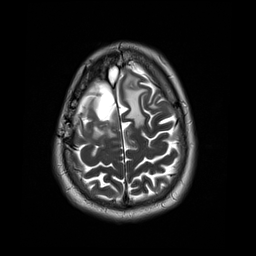
Brain MRI from a brain-tumour surgery series, one axial slice. Position 9 of 44 along the scan axis. 4 mm slice thickness. 256 × 256 image matrix, field of view 240 × 240 mm. Case-level facts recorded for this patient, not image findings: histopathology: Astrocytoma; WHO grade: 4; IDH mutation: yes; tumour location: Right Frontal.
Structures marked on this image (manually delineated by an expert):
- tumour: bounding box [x1, y1, x2, y2] px = [83, 100, 116, 139]